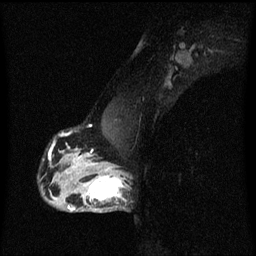
Breast MRI (dynamic contrast-enhanced), one sagittal slice; position 40 of 60 along the scan axis; dynamic contrast-enhanced series, image 2 of 3 at this slice position (ordered by acquisition); 1.5 T; TE 4.2 ms, TR 8.4 ms; 256 × 256 image matrix. Patient: female, 40 years.
Structures marked on this image (semi-automatic segmentation, software-assisted and operator-edited):
- analysis volume of interest (the breast-tissue region the enhancement analysis was run in; not a lesion): bounding box (x1, y1, x2, y2) in pixels: (76, 172, 130, 213)
- tumour enhancement mask (voxels above the 70 % enhancement threshold inside the analysis volume of interest): (76, 172, 126, 201)